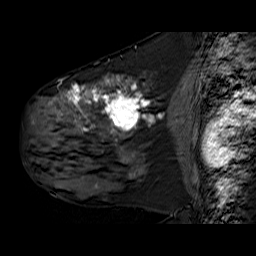
Breast MRI (dynamic contrast-enhanced), one sagittal slice; dynamic contrast-enhanced series, time point 2 of 6 at this slice position (early post-contrast); 1.5 T; TE 6.3 ms, TR 32.9 ms; 4 mm slice thickness; 256 × 256 image matrix, field of view 200 × 200 mm. Female patient. From the clinical record (not read from this slice): setting: breast cancer imaged before/during neoadjuvant chemotherapy; receptor status: HER2-positive.
Annotated regions visible in this slice (semi-automatically segmented with operator editing):
- analysis volume of interest (the breast-tissue region the enhancement analysis was run in; not a lesion): bounding box <30,78,173,180> (left, top, right, bottom; pixels)
- tumour enhancement mask (voxels above the 100 % enhancement threshold inside the analysis volume of interest): <57,78,150,177>